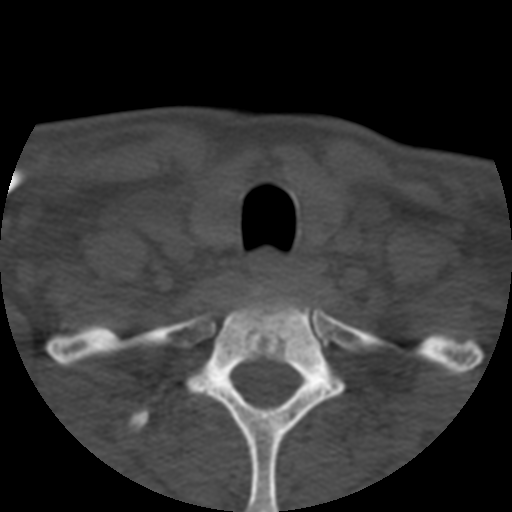
CT including the spine, one axial slice. Position 448 of 508 along the scan axis. Reconstruction kernel STANDARD. 120 kVp. Bone window (W 1800 / L 400 HU). 1.25 mm slice thickness. 512 × 512 image matrix. Patient age 57 years. Case-level facts recorded for this patient, not image findings: primary cancer: prostate.
Structures marked on this image (semi-automatically segmented with operator editing):
- T1 vertebra: bounding box <129,286,381,512> (left, top, right, bottom; pixels)